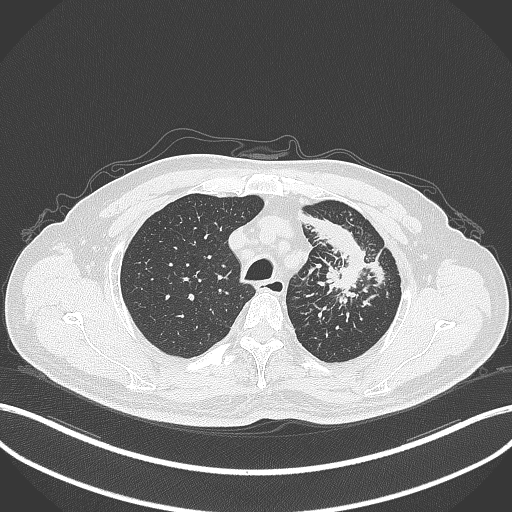
Chest CT, one axial slice. Position 285 of 386 along the scan axis. Reconstruction kernel B70f. 120 kVp. Lung window (W 1500 / L -600 HU). 1 mm slice thickness. 512 × 512 image matrix. Patient: male, 69 years. Case-level facts recorded for this patient, not image findings: clinical TNM (as recorded): T2a N2 M0.
Outlined on this slice (rectangle marked by the reading radiologist):
- lung tumour (recorded histology: adenocarcinoma): bounding box [x1, y1, x2, y2] px = [303, 207, 396, 297]